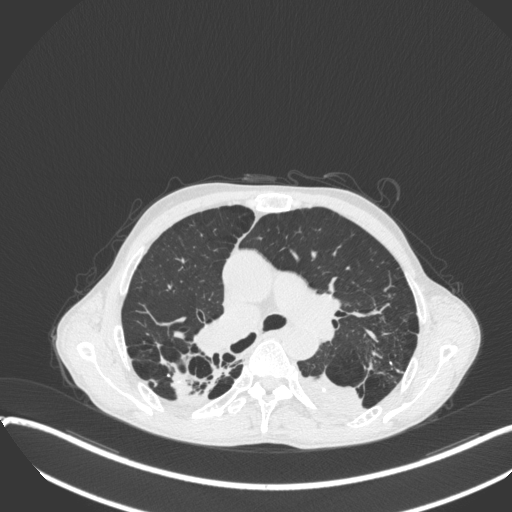
Chest CT, one axial slice. Position 244 of 400 along the scan axis. Reconstruction kernel B31f. 120 kVp. Lung window (W 1500 / L -600 HU). 1 mm slice thickness. 512 × 512 image matrix, field of view 400 × 400 mm. Male patient, age 57 years. From the clinical record (not read from this slice): clinical TNM (as recorded): T4 N0 M0.
Annotated regions visible in this slice (rectangle marked by the reading radiologist):
- lung tumour (recorded histology: squamous cell carcinoma): box from (x=299, y=374) to (x=368, y=420) px